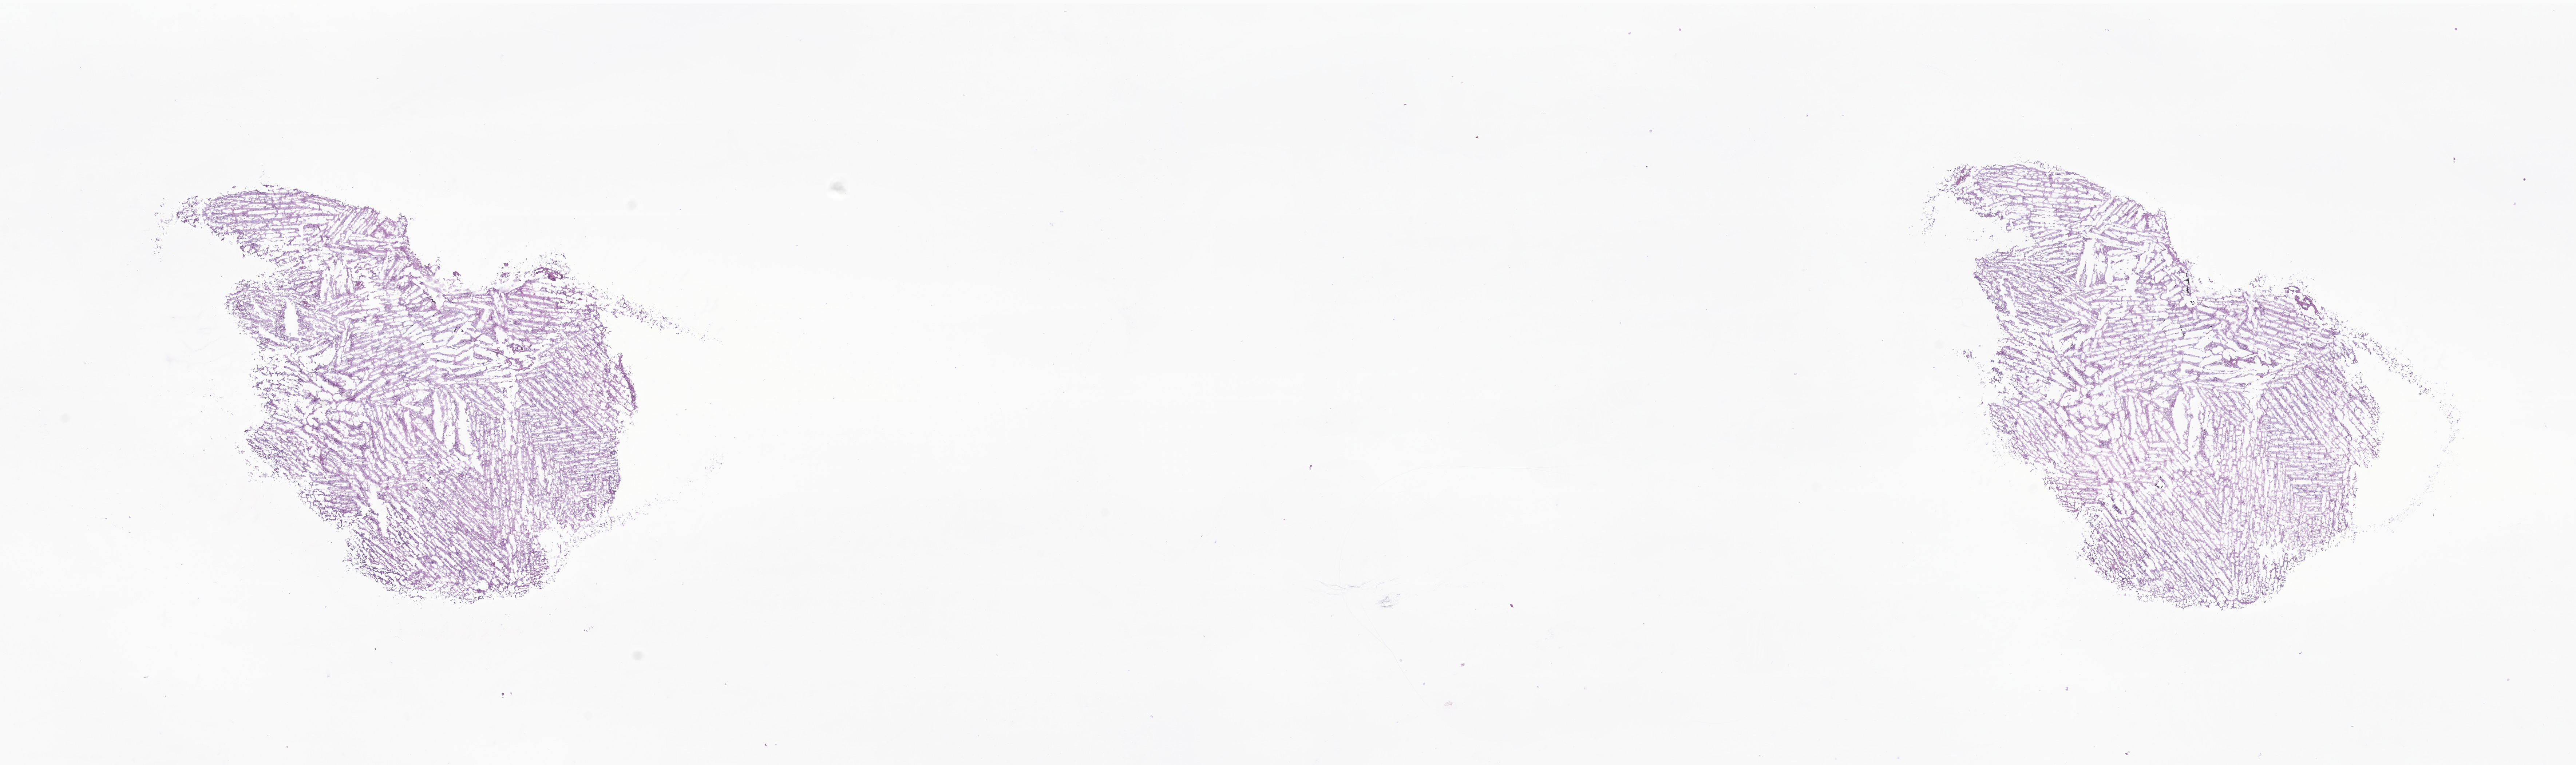
H&E whole-slide image of tumor tissue from the brain, a low-resolution overview of the entire scanned area, about 29.8 x 8.9 mm; cryosection (OCT / tissue freezing medium). Female patient, age 455 days (about 1.2 years).
- recorded diagnosis: Ependymoma, NOS